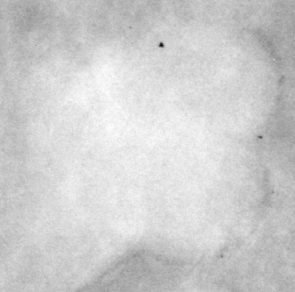
Region of interest cut from a scanned film mammogram (one marked finding), right breast, CC view, BI-RADS breast density category 2 (scale 1–4).
Mass, shape lobulated, margins circumscribed / ill defined; BI-RADS assessment category 4; pathology result (as recorded, not read from the image): malignant.